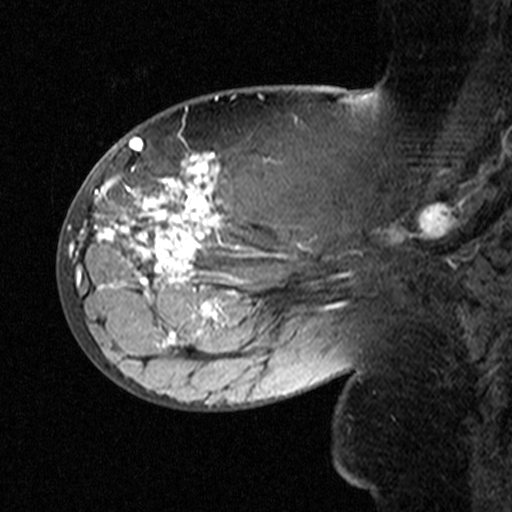
Breast MRI (dynamic contrast-enhanced), one sagittal slice; position 19 of 44 along the scan axis; dynamic contrast-enhanced study with each time point stored as its own series, time point 2 of 3 at this slice position (early post-contrast, ordered by acquisition time); 1.5 T; TE 4.5 ms, TR 11 ms; 3 mm slice thickness; 512 × 512 image matrix. Patient: female, 53 years. Case-level facts recorded for this patient, not image findings: setting: breast cancer imaged before/during neoadjuvant chemotherapy; receptor status: HR-positive, HER2-negative.
Outlined on this slice (semi-automatically segmented with operator editing):
- analysis volume of interest (the breast-tissue region the enhancement analysis was run in; not a lesion): bounding box (x1, y1, x2, y2) in pixels: (76, 140, 311, 353)
- tumour enhancement mask (voxels above the 90 % enhancement threshold inside the analysis volume of interest): (76, 152, 255, 344)